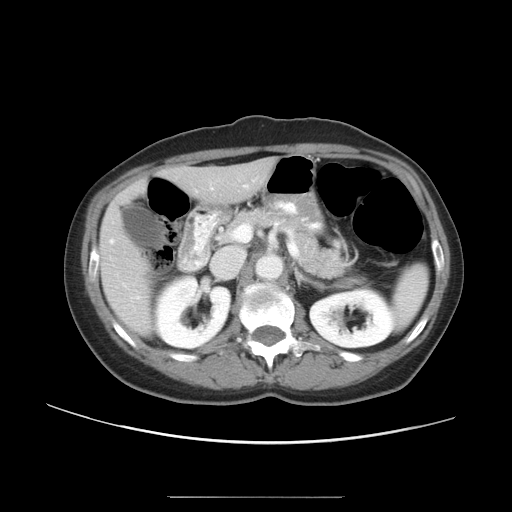
Contrast-enhanced abdominal CT, one axial slice; position 25 of 50 along the scan axis; 120 kVp; intravenous contrast given; soft-tissue window (W 400 / L 40 HU); 5 mm slice thickness; 512 × 512 image matrix, field of view 389 × 389 mm. Female patient, age 58 years. From the clinical record (not read from this slice): diagnosis: colorectal cancer liver metastases, imaged before liver resection; multiple liver metastases: yes; largest metastasis: 7.3 cm; disease in both lobes: yes.
Annotated regions visible in this slice (manually delineated by an expert):
- hepatic veins: box from (x=110, y=240) to (x=114, y=243) px
- liver: (x=101, y=161)–(x=271, y=333)
- planned liver remnant (the part of the liver to remain after resection): (x=166, y=161)–(x=271, y=202)